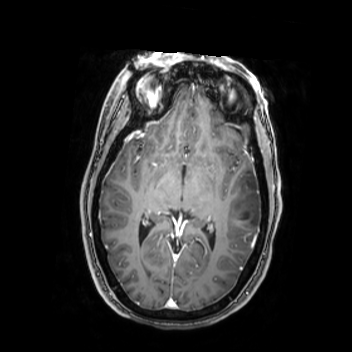
Brain MRI from a brain-tumour surgery series, one axial slice. Slice 148 of 350 in the series (ordered by position). T1-weighted post-contrast. 0.9 mm slice thickness. 352 × 352 image matrix. From the clinical record (not read from this slice): histopathology: Oligodendroglioma; WHO grade: 2; IDH mutation: yes.
Annotated regions visible in this slice (manually delineated by an expert):
- tumour: bounding box [x1, y1, x2, y2] px = [224, 174, 262, 230]